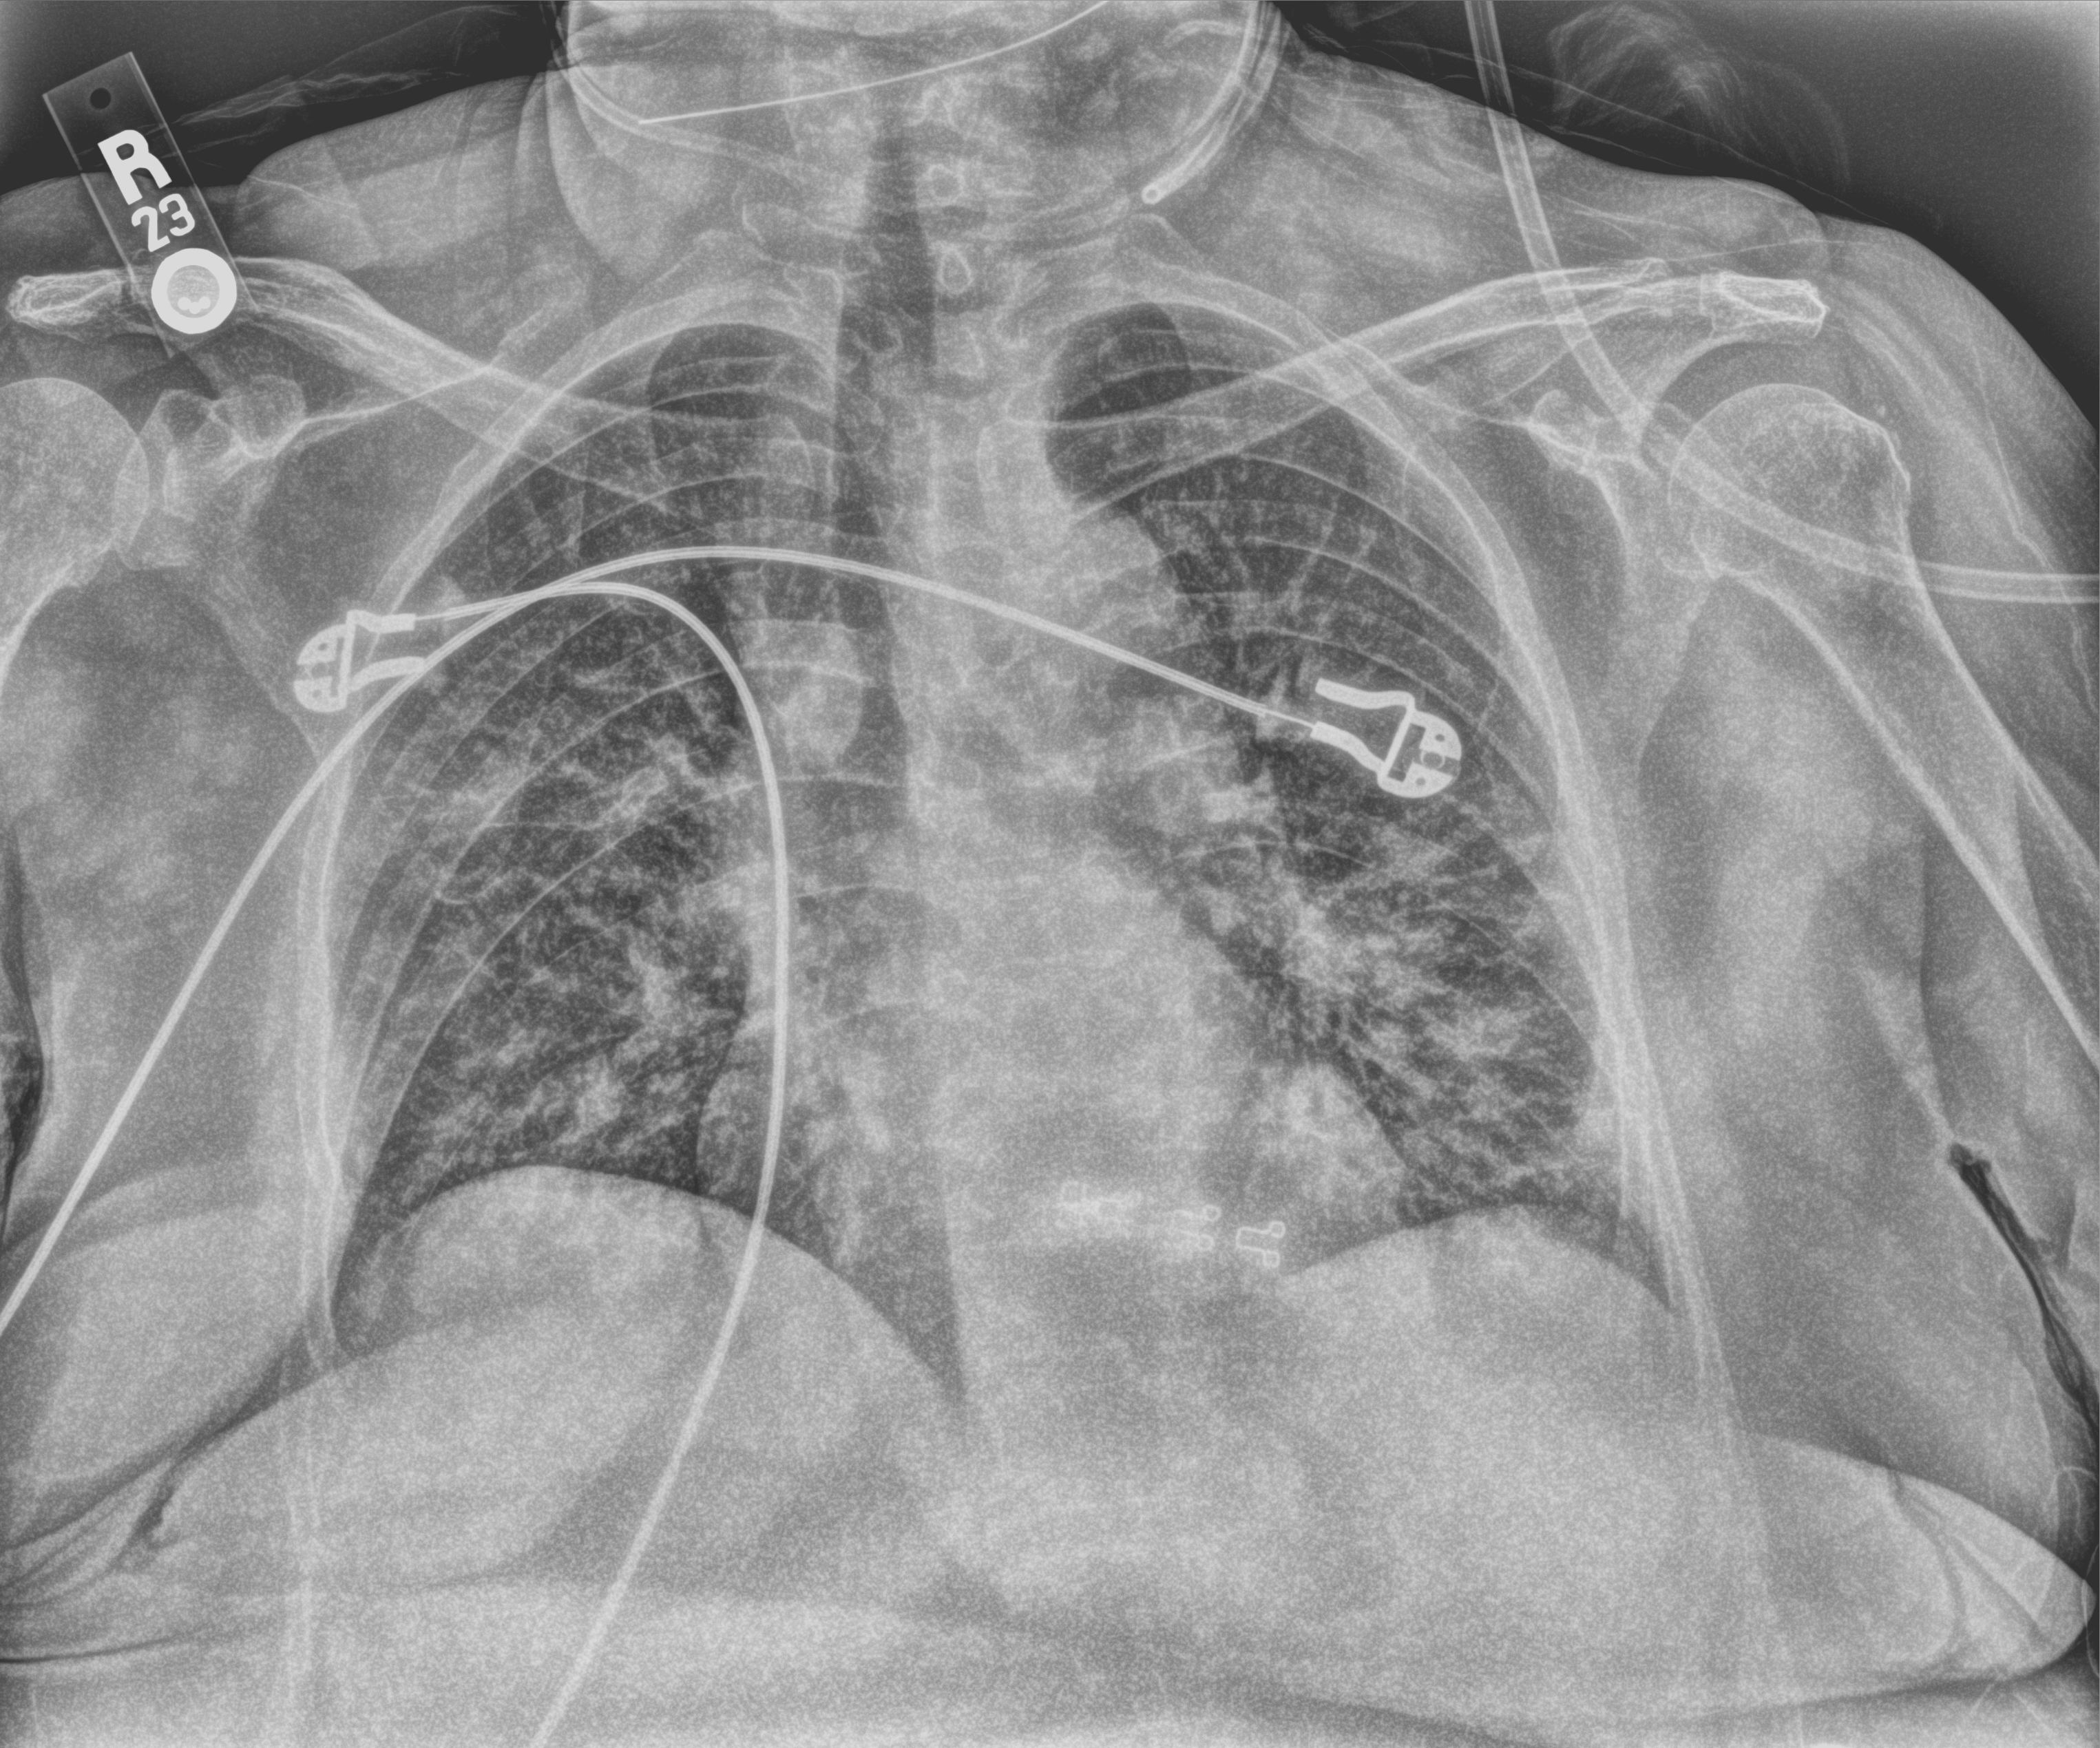
Portable chest radiograph, anteroposterior (AP) projection. Patient hospitalised with COVID-19; female, aged 60–74 years.
Hospital-stay facts (about this admission, not read from this image; timing relative to this image not recorded):
- hypertension (admission record): yes
- admitted to intensive care during this hospital stay: yes